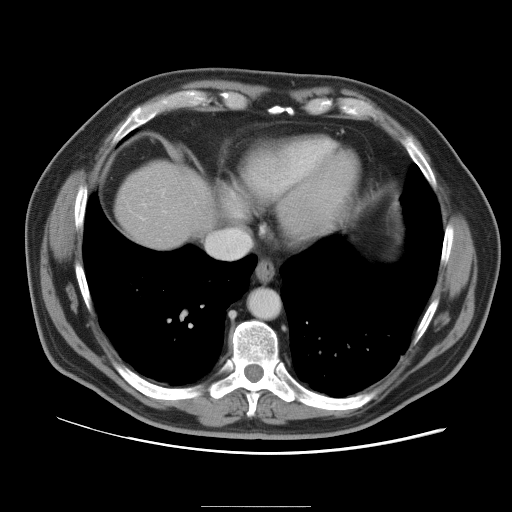
Contrast-enhanced abdominal CT, one axial slice; position 92 of 105 along the scan axis; 120 kVp; intravenous contrast given; soft-tissue window (W 400 / L 40 HU); 5 mm slice thickness; 512 × 512 image matrix. Male patient, age 64 years. Case-level facts recorded for this patient, not image findings: diagnosis: colorectal cancer liver metastases, imaged before liver resection; multiple liver metastases: yes; largest metastasis: 3 cm; disease in both lobes: yes.
Structures marked on this image (outlined manually by an expert reader):
- liver: bounding box (x1, y1, x2, y2) in pixels: (116, 161, 210, 248)
- planned liver remnant (the part of the liver to remain after resection): (116, 163, 208, 248)